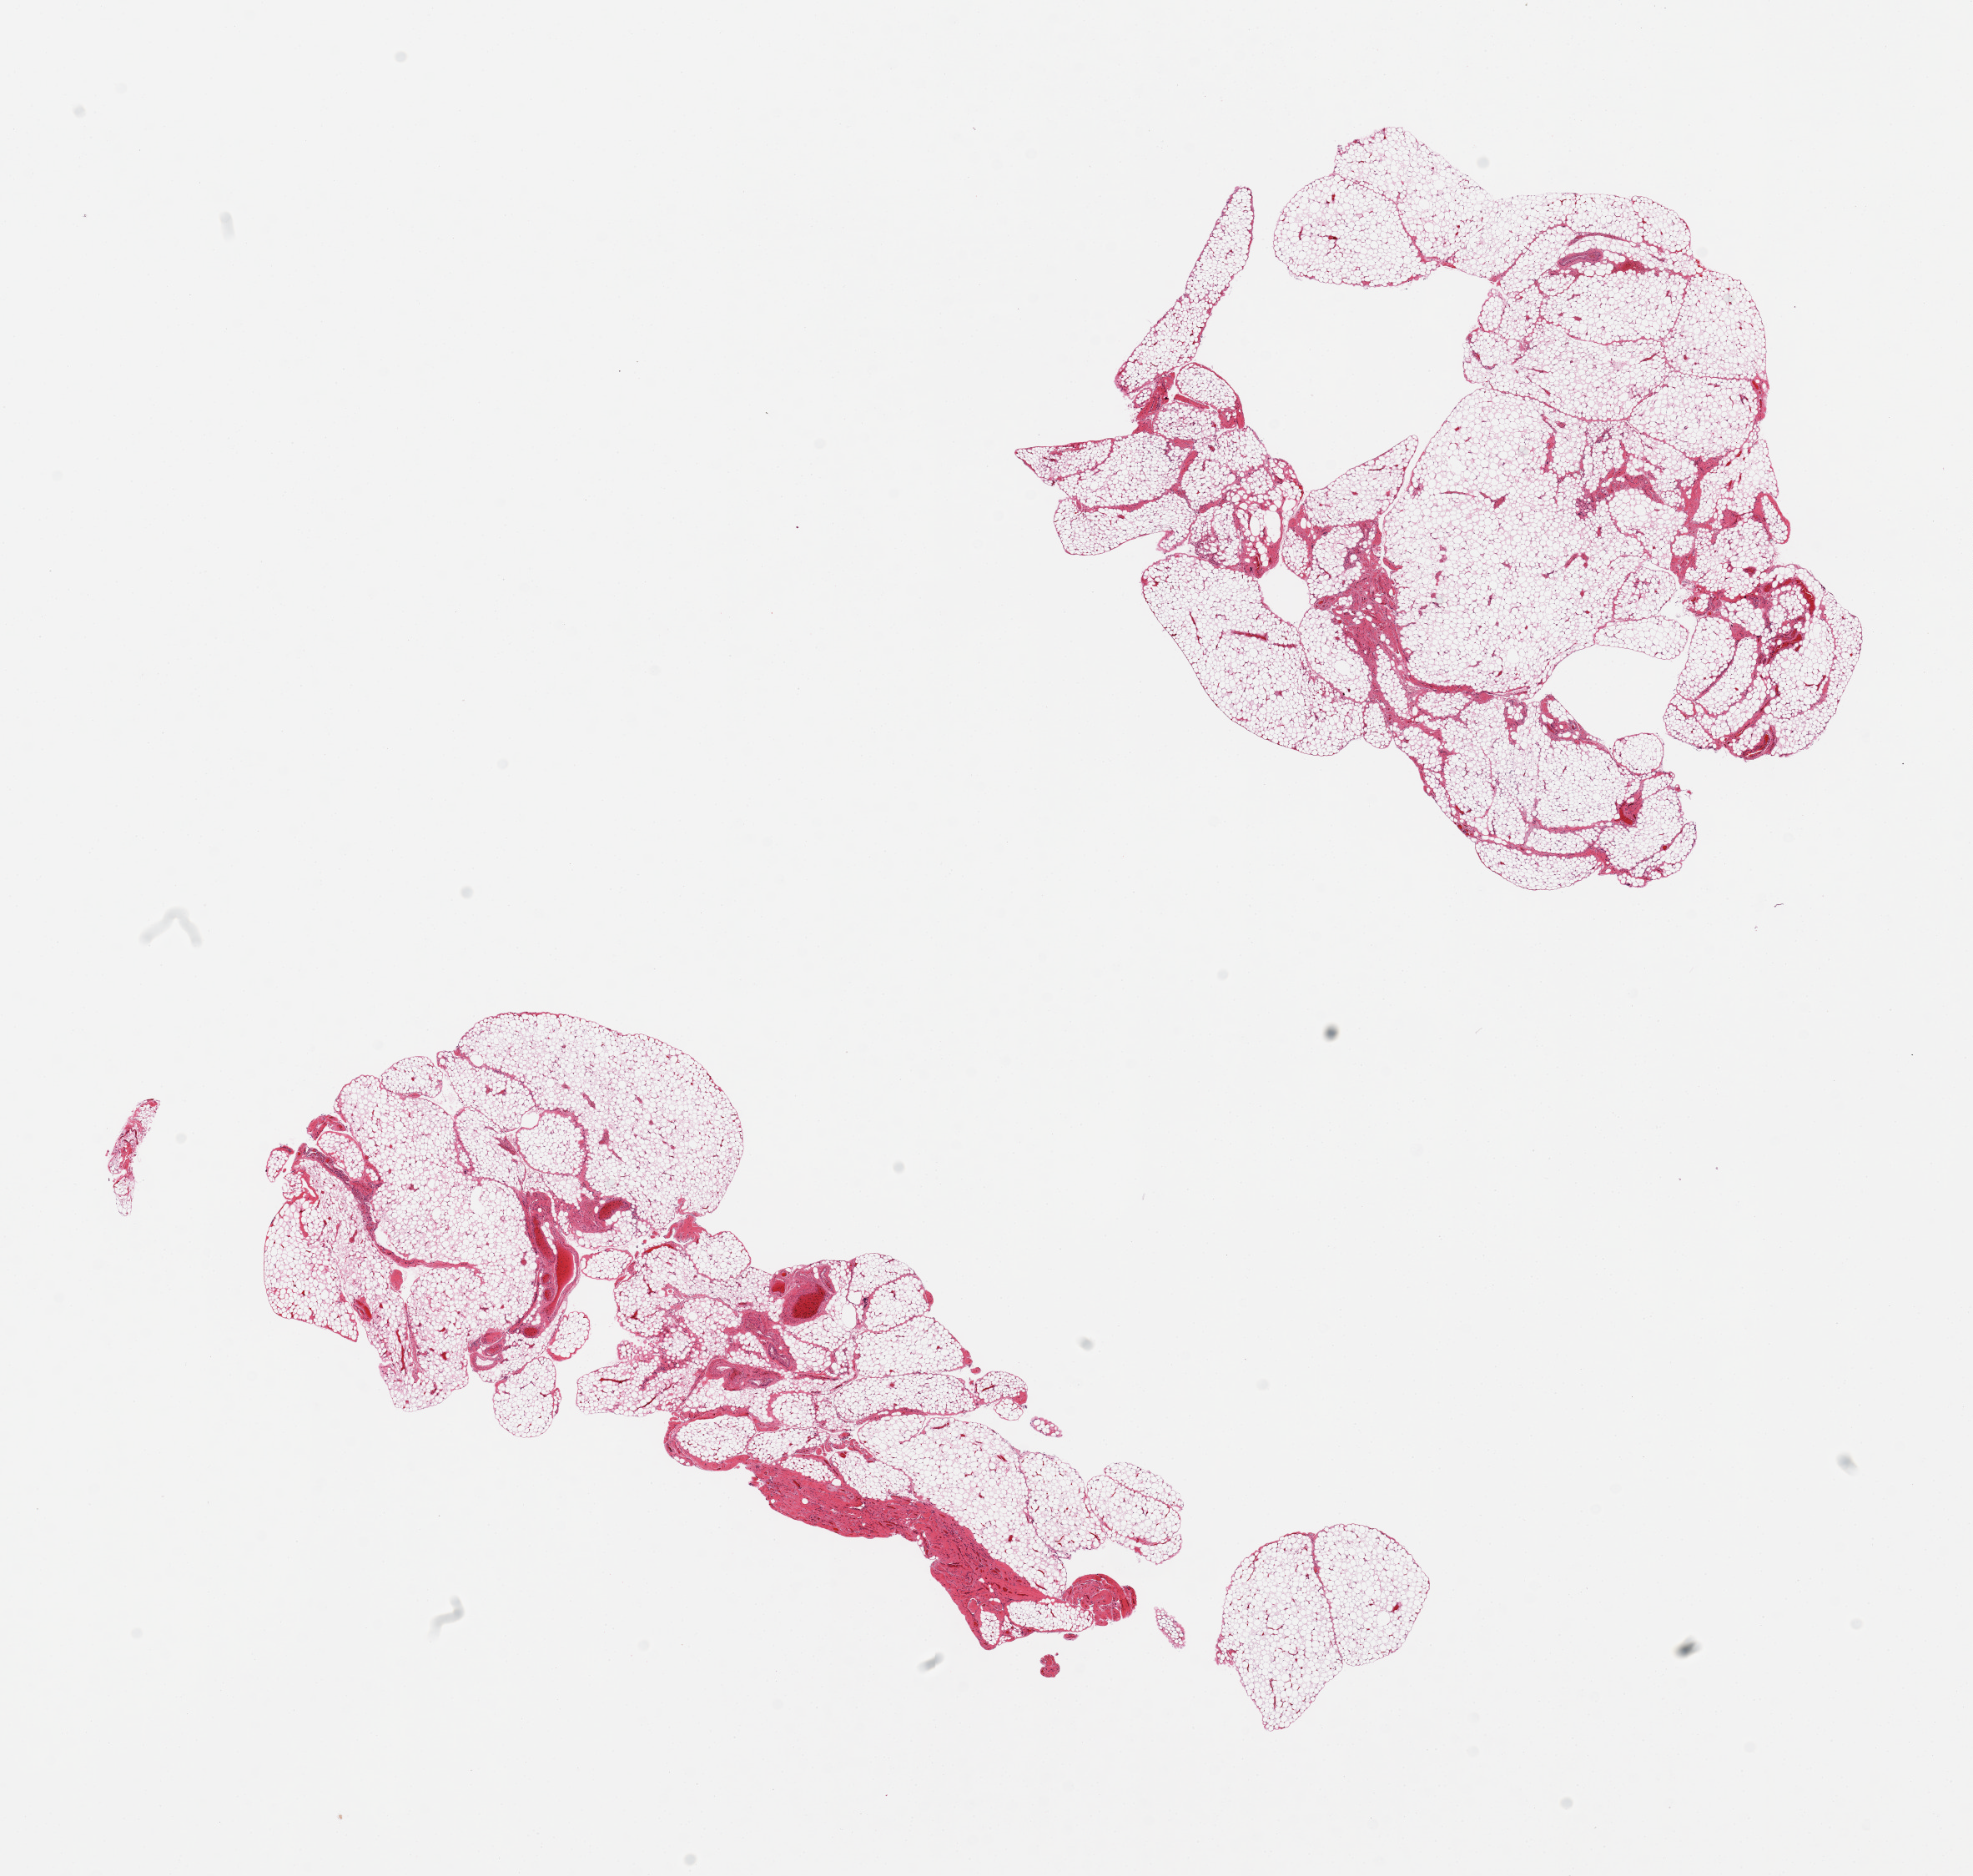
Digitized haematoxylin and eosin-stained section, a low-resolution overview of the entire scanned area, about 18.7 x 17.8 mm, PAXgene-fixed paraffin-embedded (PFPE) section, target tissue: omentum, donor tissue sample. Donor sex: female.
Review note (as recorded): 2 pieces.